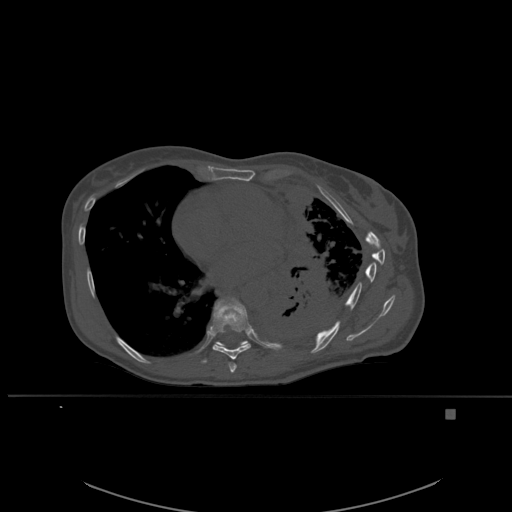
CT including the spine, one axial slice. Slice 347 of 537 in the series (ordered by position). Bone window (W 1800 / L 400 HU). 512 × 512 image matrix. Patient: female, 45 years. From the clinical record (not read from this slice): primary cancer: lung.
Outlined on this slice (semi-automatic segmentation, software-assisted and operator-edited):
- T7 vertebra: bounding box (x1, y1, x2, y2) in pixels: (228, 362, 237, 373)
- T8 vertebra: (202, 297, 251, 363)
- T9 vertebra: (213, 307, 249, 348)